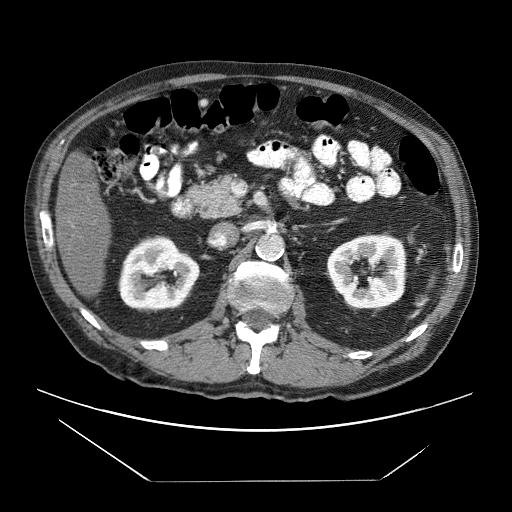
Contrast-enhanced abdominal CT (liver protocol), one axial slice. Position 18 of 83 along the scan axis. Reconstruction kernel STANDARD. 120 kVp. Soft-tissue window (W 400 / L 40 HU). 2.5 mm slice thickness. 512 × 512 image matrix, field of view 420 × 420 mm. Case-level facts recorded for this patient, not image findings: diagnosis: hepatocellular carcinoma (patient treated with transarterial chemoembolisation; whether this scan precedes or follows treatment is not stated here); TNM stage (as recorded): Stage-IVB; Child-Pugh class: B; tumour differentiation: poorly differentiated; tumour nodularity: uninodular.
Structures marked on this image (semi-automatic segmentation, software-assisted and operator-edited):
- liver parenchyma outside the tumour (the mass and vessels are separate outlines, so this box may not span the whole liver): bounding box [x1, y1, x2, y2] px = [54, 152, 110, 297]